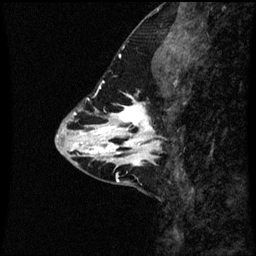
Breast MRI (dynamic contrast-enhanced), one sagittal slice. Position 21 of 60 along the scan axis. Dynamic contrast-enhanced series, image 2 of 3 at this slice position (ordered by acquisition). 1.5 T. TE 4.2 ms, TR 8.9 ms. 2 mm slice thickness. 256 × 256 image matrix, field of view 200 × 200 mm. Patient: female, 43 years. Case-level facts recorded for this patient, not image findings: setting: breast cancer imaged before/during neoadjuvant chemotherapy; receptor status: HR-positive, HER2-negative.
Outlined on this slice (semi-automatically segmented with operator editing):
- analysis volume of interest (the breast-tissue region the enhancement analysis was run in; not a lesion): bounding box [x1, y1, x2, y2] px = [110, 100, 174, 163]
- tumour enhancement mask (voxels above the 70 % enhancement threshold inside the analysis volume of interest): [110, 100, 159, 163]